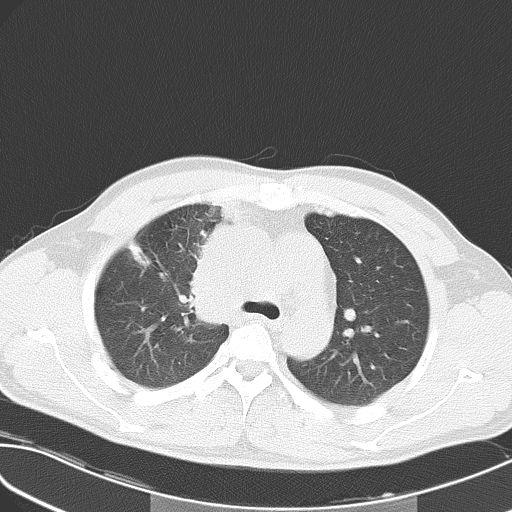
Chest CT, one axial slice. Slice 39 of 55 in the series (ordered by position). Reconstruction kernel B70f. 120 kVp. Lung window (W 1500 / L -600 HU). 512 × 512 image matrix, field of view 346 × 346 mm. Male patient, age 32 years. Case-level facts recorded for this patient, not image findings: clinical TNM (as recorded): T4 N3 M0.
Annotated regions visible in this slice (rectangle marked by the reading radiologist):
- lung tumour (recorded histology: small cell carcinoma): box from (x=183, y=214) to (x=234, y=327) px